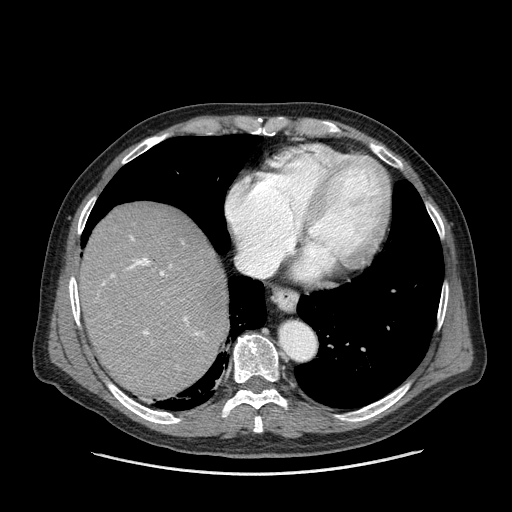
Contrast-enhanced abdominal CT (liver protocol), one axial slice. Position 132 of 180 along the scan axis. 120 kVp. One of 2 acquisitions stored at this slice position. Soft-tissue window (W 400 / L 40 HU). 512 × 512 image matrix, field of view 420 × 420 mm. From the clinical record (not read from this slice): diagnosis: hepatocellular carcinoma (patient treated with transarterial chemoembolisation; whether this scan precedes or follows treatment is not stated here); TNM stage (as recorded): Stage-II; Child-Pugh class: A; tumour differentiation: well differentiated; tumour nodularity: multinodular.
Outlined on this slice (semi-automatic segmentation, software-assisted and operator-edited):
- abdominal aorta: bounding box <281,323,316,360> (left, top, right, bottom; pixels)
- liver parenchyma outside the tumour (the mass and vessels are separate outlines, so this box may not span the whole liver): <80,202,228,396>
- liver vessels: <103,236,199,335>